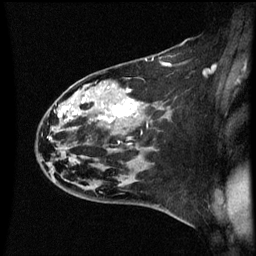
Breast MRI (dynamic contrast-enhanced), one sagittal slice; position 38 of 60 along the scan axis; dynamic contrast-enhanced series, image 2 of 3 at this slice position (ordered by acquisition); 1.5 T; TE 4.2 ms, TR 8.9 ms; 2 mm slice thickness; 256 × 256 image matrix, field of view 200 × 200 mm. Patient: female, 44 years. Case-level facts recorded for this patient, not image findings: setting: breast cancer imaged before/during neoadjuvant chemotherapy; receptor status: HR-positive, HER2-negative.
Annotated regions visible in this slice (semi-automatic segmentation, software-assisted and operator-edited):
- analysis volume of interest (the breast-tissue region the enhancement analysis was run in; not a lesion): box from (x=43, y=78) to (x=153, y=189) px
- tumour enhancement mask (voxels above the 70 % enhancement threshold inside the analysis volume of interest): (x=64, y=100)–(x=136, y=121)